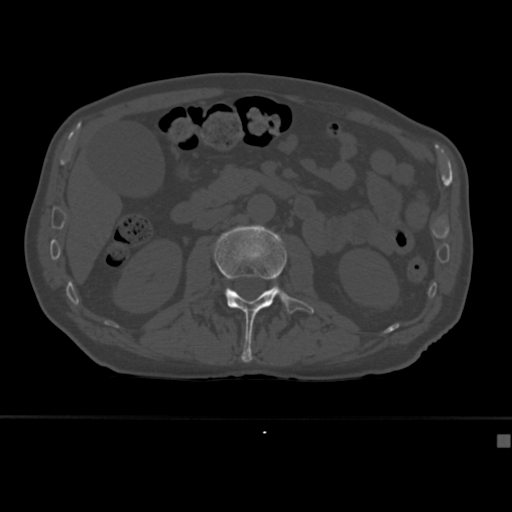
CT including the spine, one axial slice. Position 147 of 430 along the scan axis. Reconstruction kernel Br40s. Bone window (W 1800 / L 400 HU). 1.5 mm slice thickness. 512 × 512 image matrix, field of view 337 × 337 mm. Patient: male, 64 years. From the clinical record (not read from this slice): primary cancer: uterus; vertebrae with lytic lesions (as recorded): T1, T4, T5, T7, L5.
Outlined on this slice (semi-automatic segmentation, software-assisted and operator-edited):
- L2 vertebra: bounding box <214,225,314,363> (left, top, right, bottom; pixels)